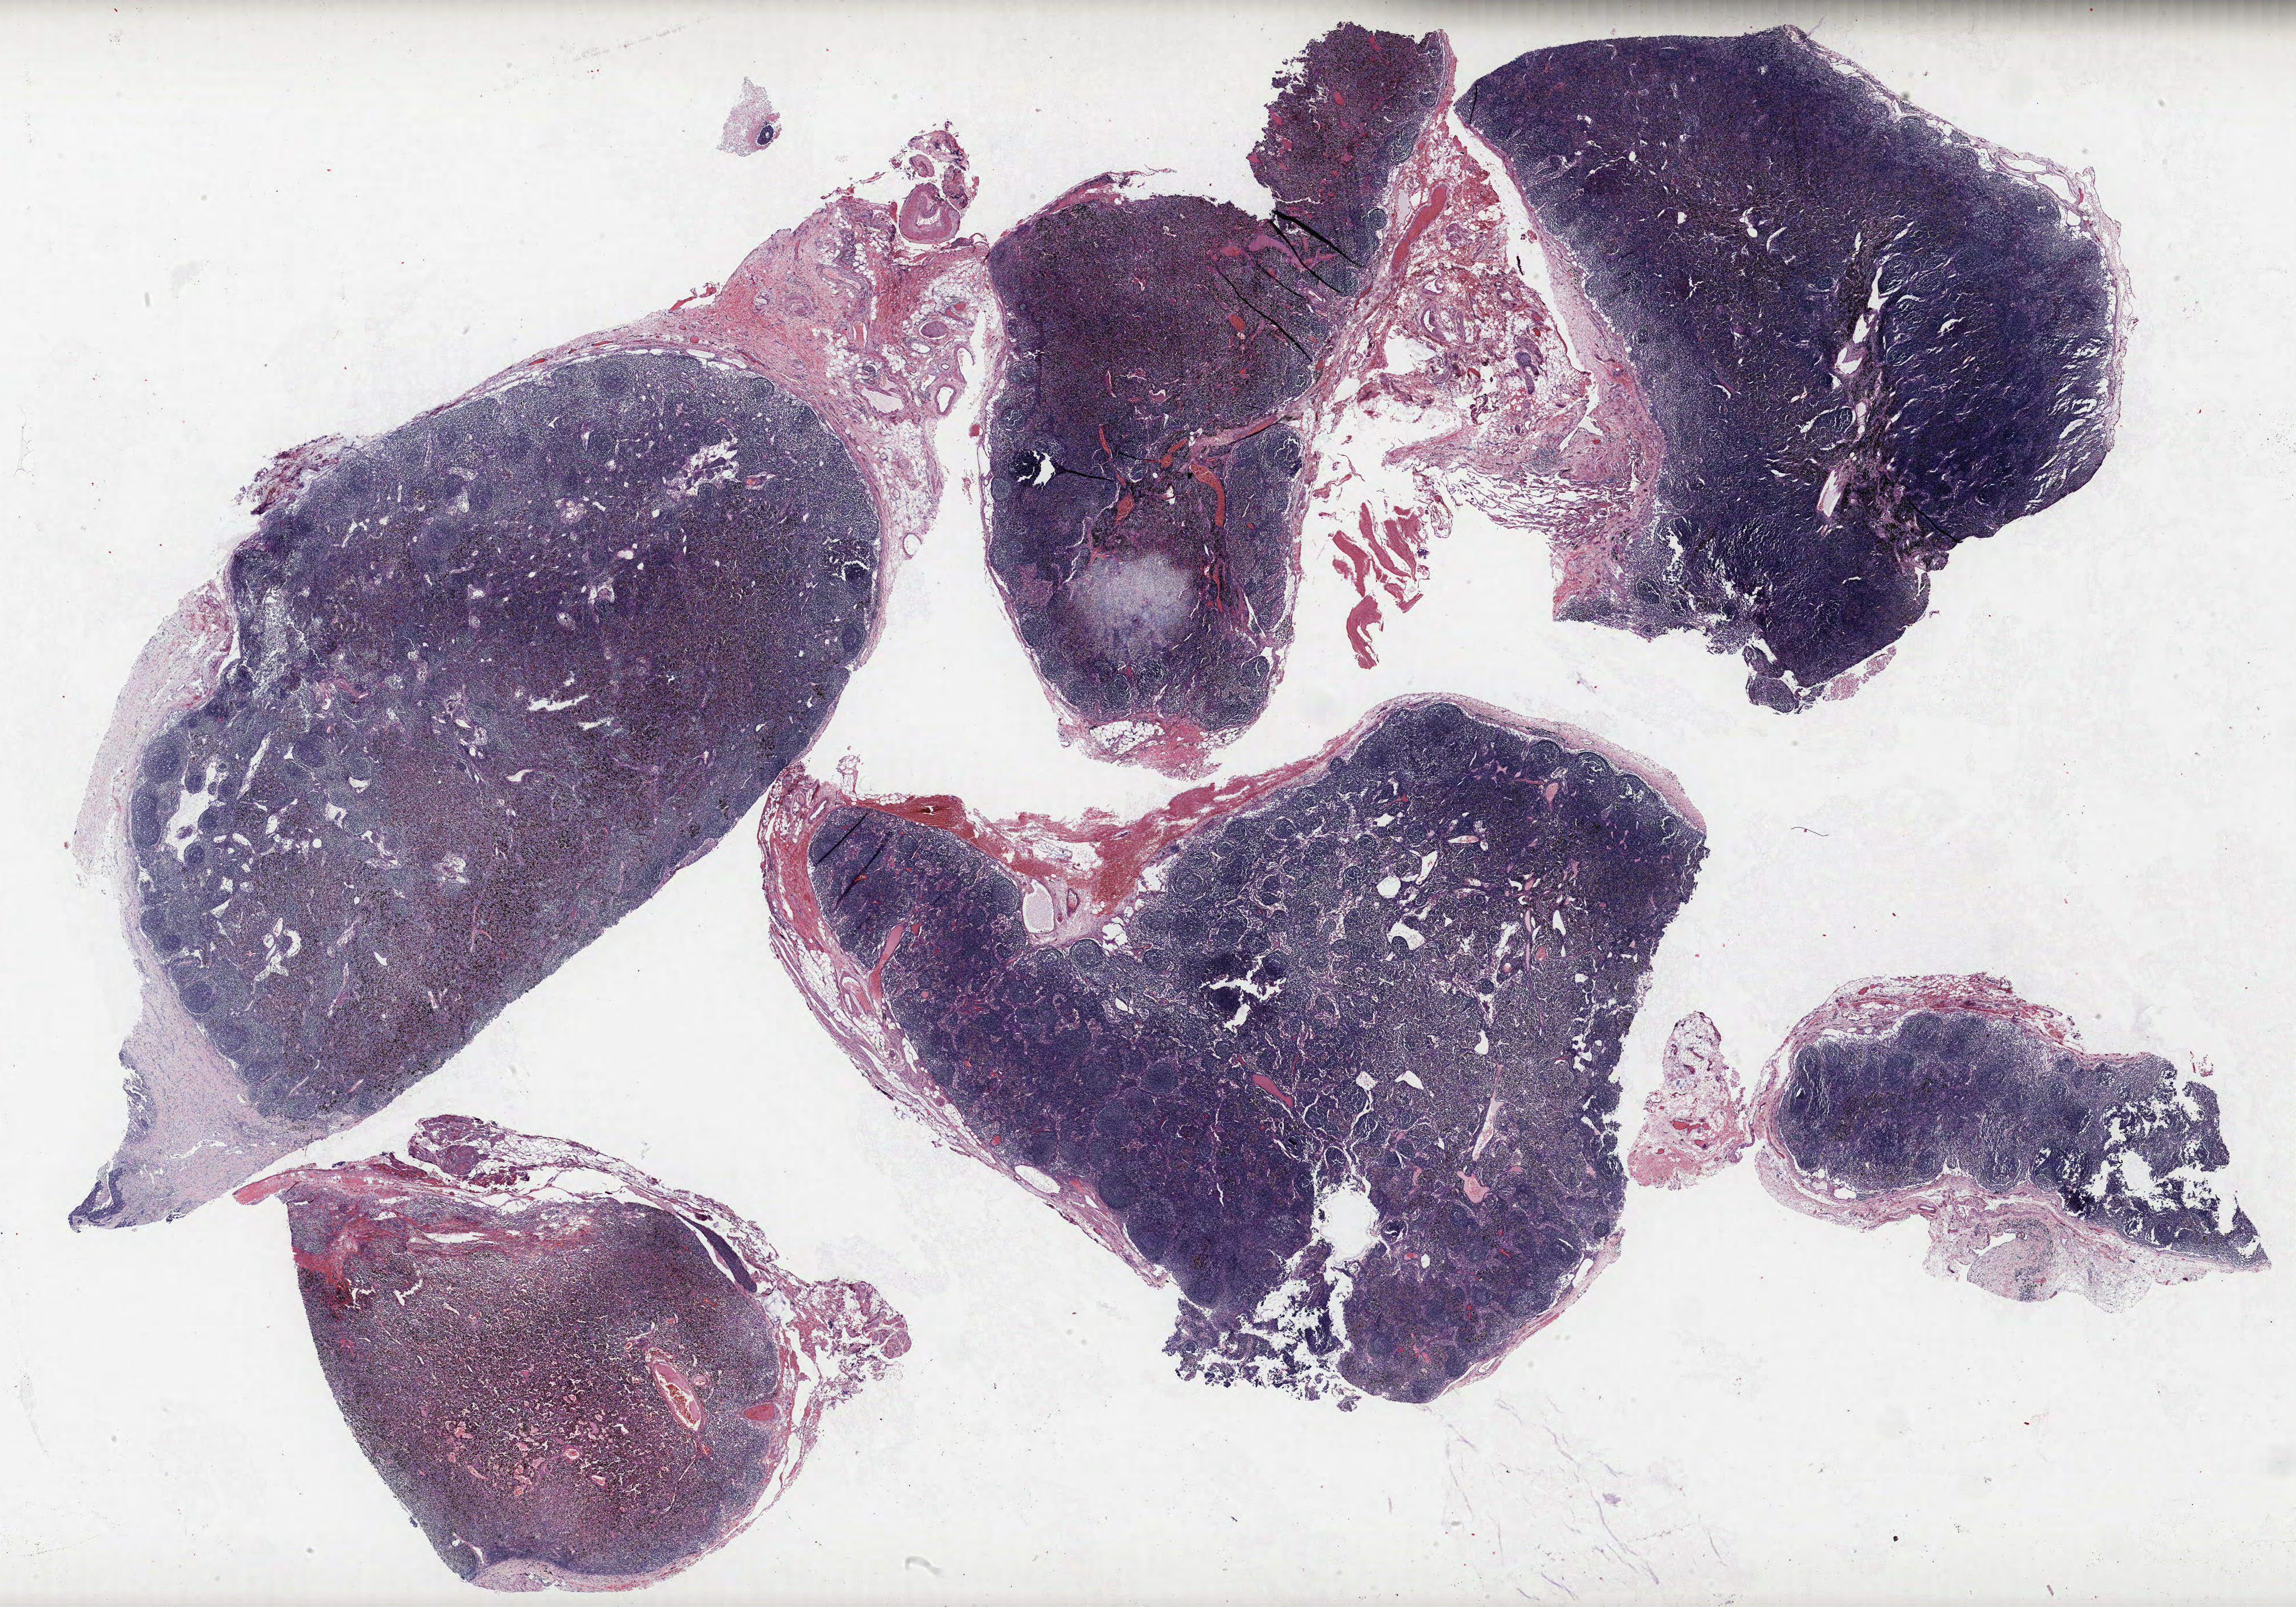
H&E whole-slide image, low-resolution overview of the scanned area, about 31.9 x 22.3 mm (slide scanned at 40x), formalin-fixed paraffin-embedded (FFPE) section, lung tissue. Male patient, aged 65 at enrolment. Current smoker at enrolment.
Participant's lung-cancer diagnosis: Adenocarcinoma, NOS (ICD-O-3 8140/3). Note: participant had 2 primary lung cancers recorded; fields above describe the first.